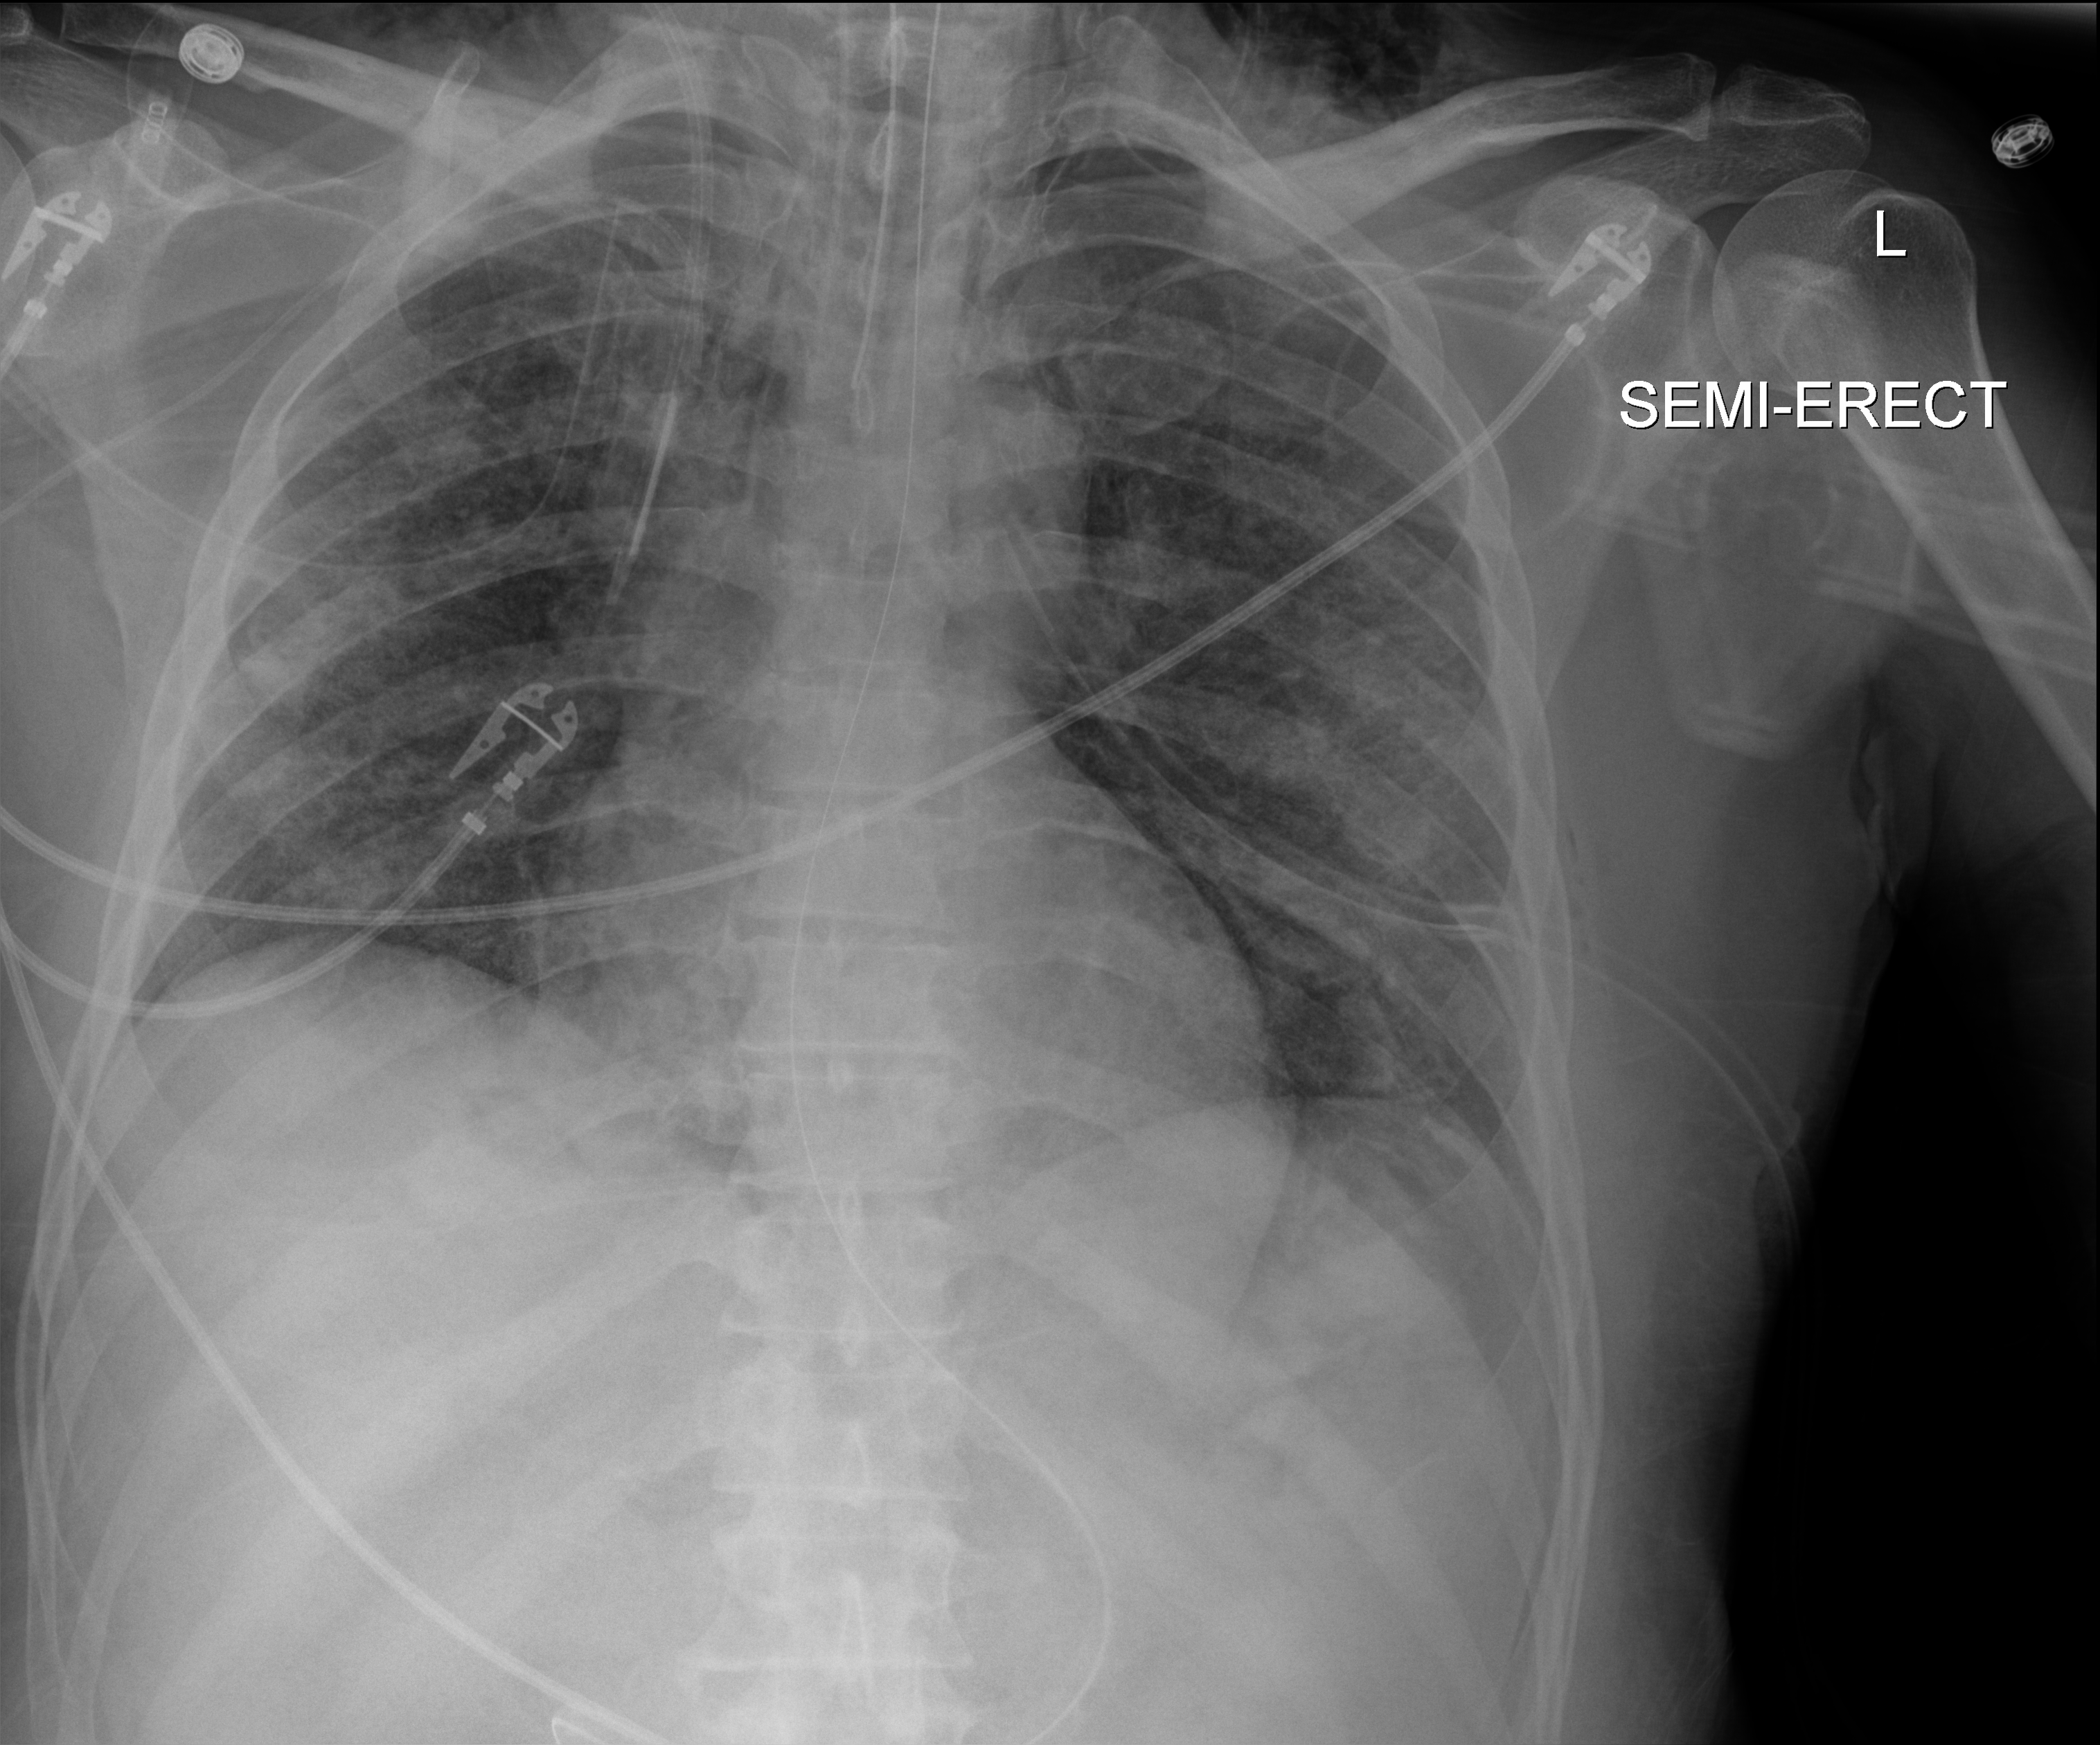
Bedside chest radiograph (digital radiography), anteroposterior (AP) projection. Male patient hospitalised with COVID-19, age 18–59 years.
From the hospital-stay record, not from the radiograph (when in the stay this image was taken is not recorded): mechanically ventilated during this hospital stay: yes; COPD (admission record): no.